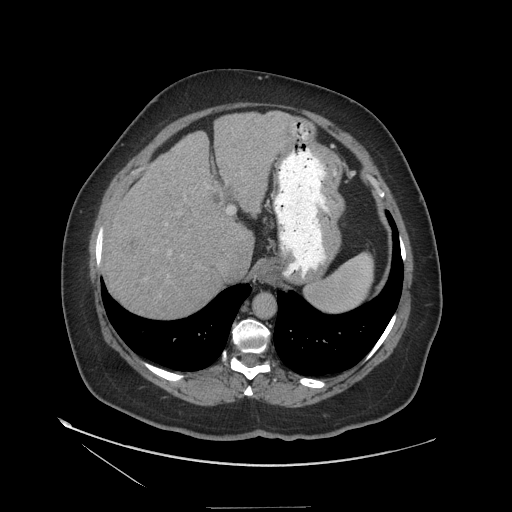
Contrast-enhanced abdominal CT (liver protocol), one axial slice. Position 90 of 127 along the scan axis. Reconstruction kernel STANDARD. Soft-tissue window (W 400 / L 40 HU). 2.5 mm slice thickness. 512 × 512 image matrix, field of view 480 × 480 mm. Case-level facts recorded for this patient, not image findings: diagnosis: hepatocellular carcinoma (patient treated with transarterial chemoembolisation; whether this scan precedes or follows treatment is not stated here); TNM stage (as recorded): Stage-II; Child-Pugh class: A; tumour nodularity: multinodular.
Outlined on this slice (semi-automatically segmented with operator editing):
- abdominal aorta: bounding box <253,293,275,318> (left, top, right, bottom; pixels)
- liver parenchyma outside the tumour (the mass and vessels are separate outlines, so this box may not span the whole liver): <104,112,298,318>
- mass: <121,237,140,257>
- liver vessels: <227,207,233,213>